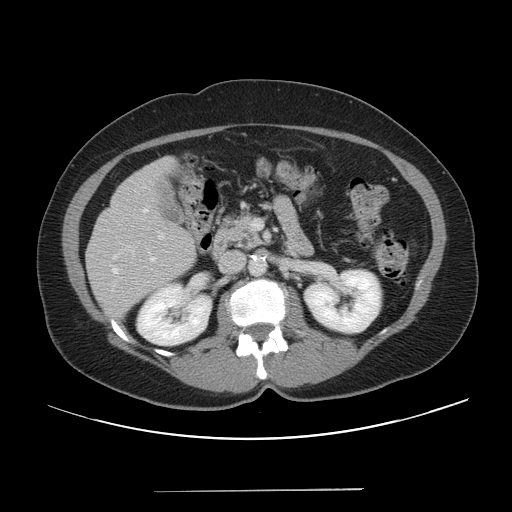
Contrast-enhanced abdominal CT, one axial slice; position 20 of 56 along the scan axis; 120 kVp; intravenous contrast given; soft-tissue window (W 400 / L 40 HU); 5 mm slice thickness; 512 × 512 image matrix, field of view 419 × 419 mm. Female patient, age 54 years. Case-level facts recorded for this patient, not image findings: diagnosis: colorectal cancer liver metastases, imaged before liver resection; multiple liver metastases: yes.
Structures marked on this image (expert manual segmentation):
- hepatic veins: box from (x=113, y=268) to (x=117, y=273) px
- liver: (x=86, y=159)–(x=196, y=321)
- planned liver remnant (the part of the liver to remain after resection): (x=158, y=159)–(x=175, y=174)
- portal vein (with intrahepatic branches): (x=159, y=221)–(x=261, y=238)